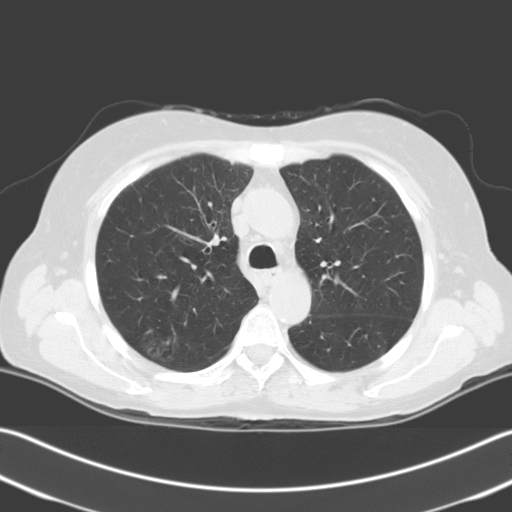
Low-dose screening chest CT, axial slice, baseline screening round, lung window (W 1500 / L -600 HU), 3.2 mm slice thickness, slice 53 of 204 in the series. Female participant, aged 67 years at enrolment. Current smoker at enrolment.
Expert reader's lesion annotation, bounding box (x1, y1, x2, y2) in pixels: (125, 325, 185, 373). The screening reader recorded 2 non-calcified nodules or masses ≥4 mm on this exam; which of them this box marks is not recorded. Official screen result: positive, change unspecified: nodule(s) >= 4 mm or enlarging nodule(s), mass(es), or other non-specific abnormalities suspicious for lung cancer. Later outcome: lung cancer diagnosed 24 days after this screen — squamous cell carcinoma, NOS, right upper lobe, stage IIIA (AJCC 6th edition), 56 mm at pathology.